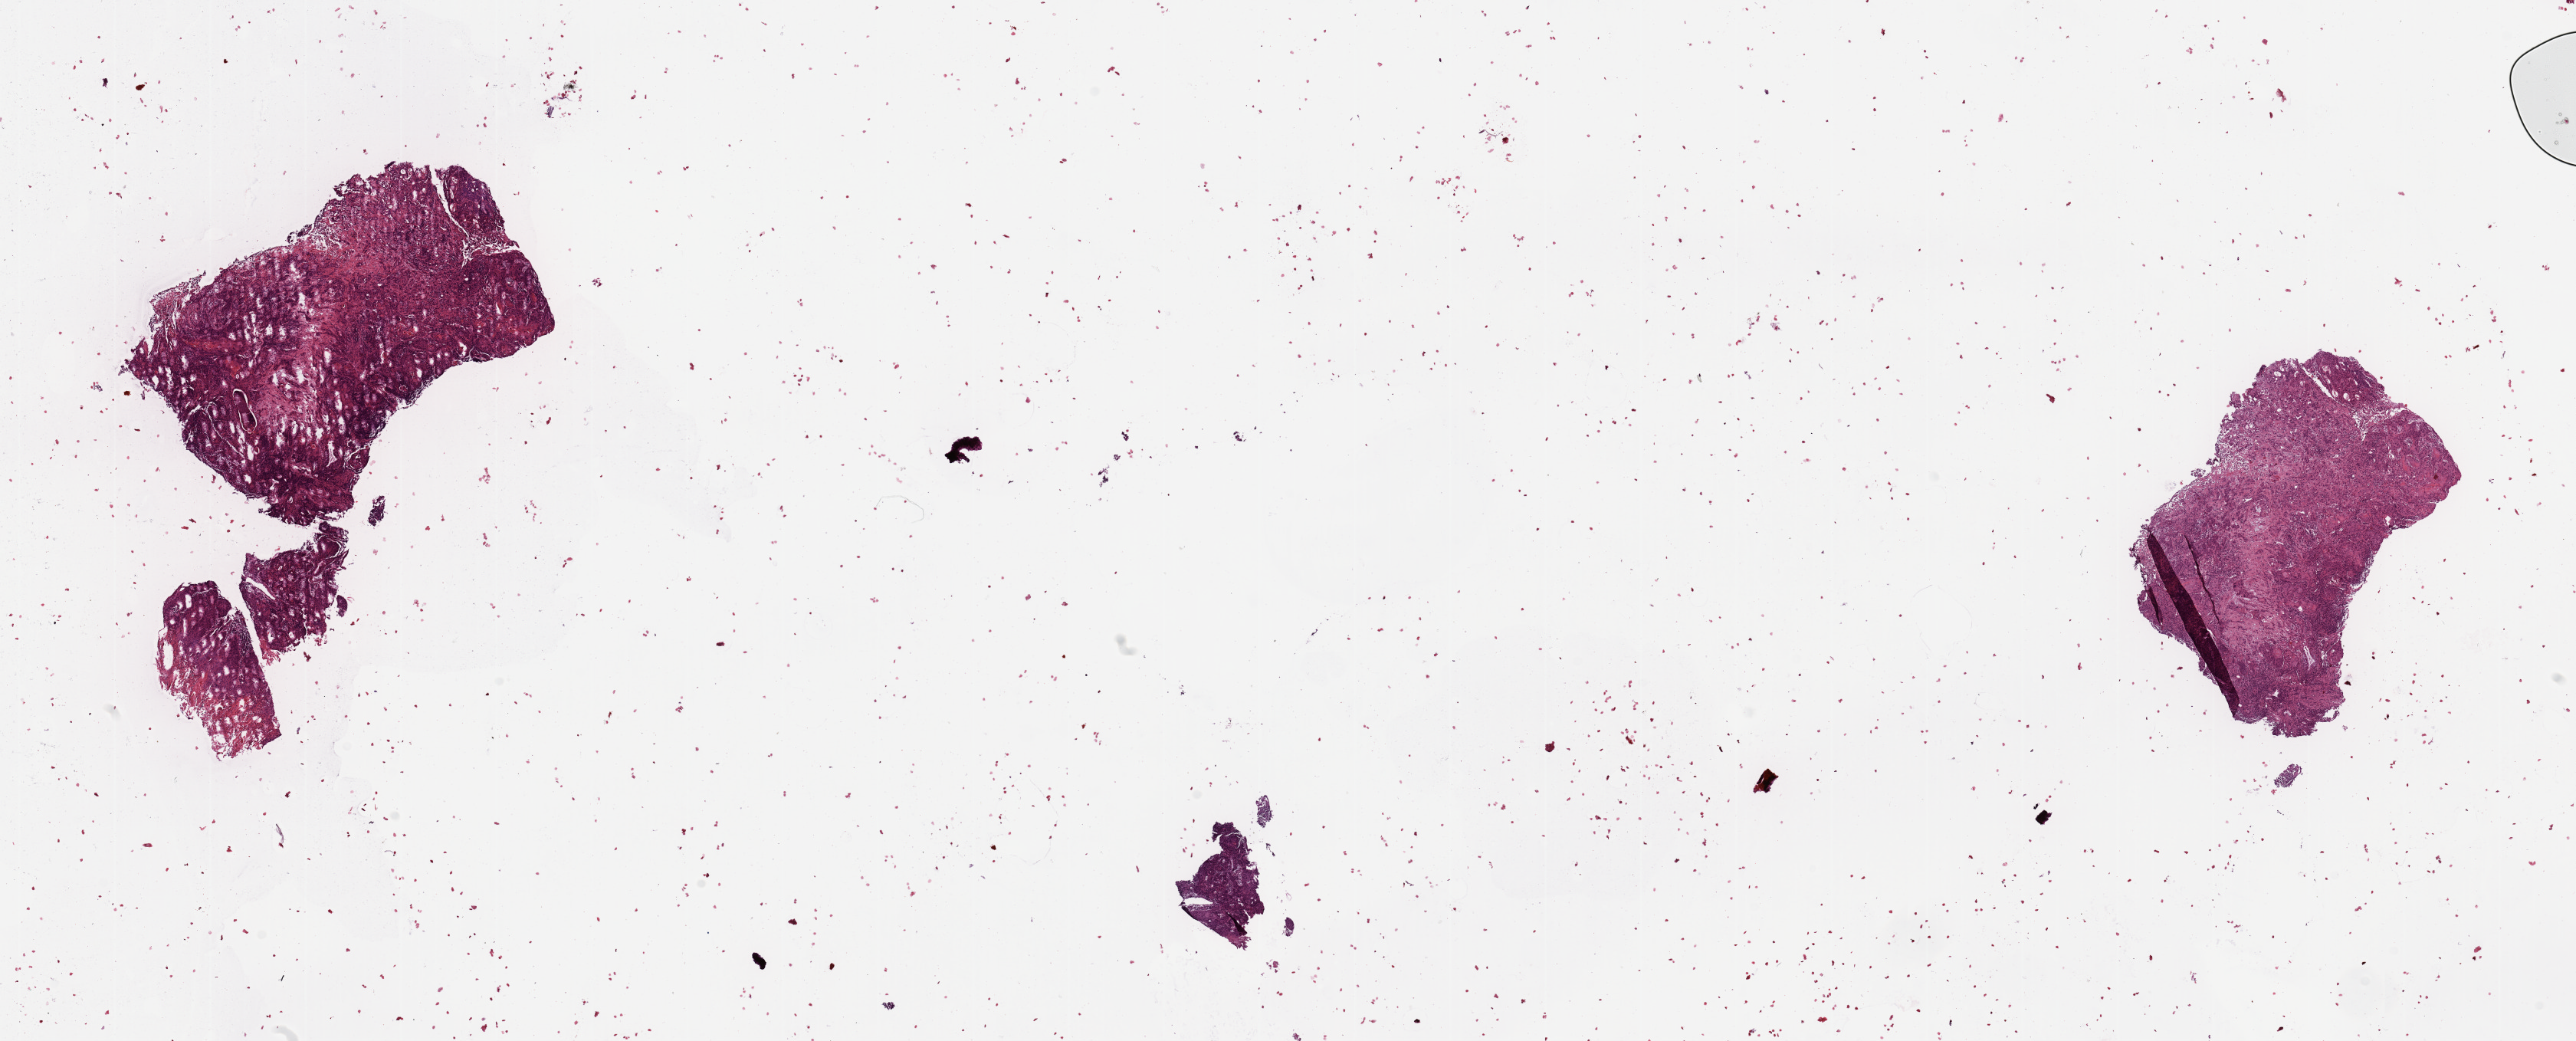
Digitized Hematoxylin and eosin (H&E) stained tissue section (whole slide), whole scanned area (about 26.6 x 10.7 mm, slide scanned at 20x) shown as a low-resolution overview, tumour tissue sample, sampled site: larynx. 71-year-old male patient. Histologic grade: G2 (moderately differentiated). Composition of this section per pathologist review: tumour nuclei 80%, necrosis 5%.
• diagnosis: Squamous cell carcinoma, NOS (larynx, NOS)
• primary tumour site (as recorded): larynx
• AJCC pathologic stage: III